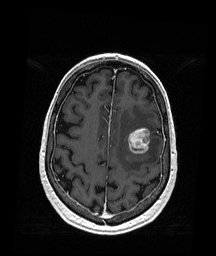
Brain MRI from a brain-tumour surgery series, one axial slice; position 56 of 176 along the scan axis; T1-weighted post-contrast; 216 × 256 image matrix, field of view 211 × 250 mm. Case-level facts recorded for this patient, not image findings: histopathology: Metastatic Melanoma; tumour location: Left Frontal.
Annotated regions visible in this slice (manually delineated by an expert):
- tumour: bounding box [x1, y1, x2, y2] px = [127, 128, 151, 154]